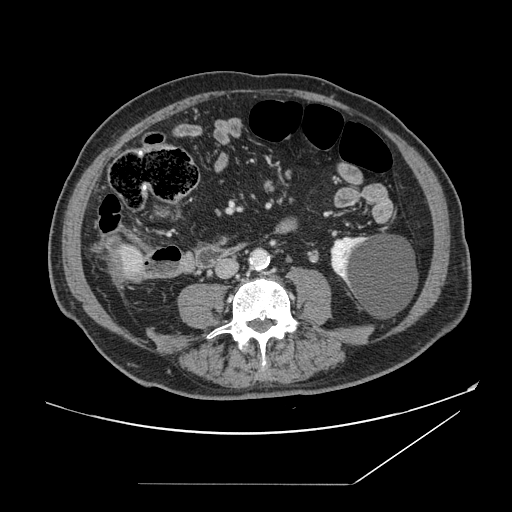
Contrast-enhanced abdominal CT, one axial slice. Slice 23 of 166 in the series (ordered by position). 120 kVp. Intravenous contrast given. Soft-tissue window (W 400 / L 40 HU). 2.5 mm slice thickness. 512 × 512 image matrix. Male patient, age 80 years. From the clinical record (not read from this slice): diagnosis: colorectal cancer liver metastases, imaged before liver resection; multiple liver metastases: no; largest metastasis: 2.2 cm; disease in both lobes: no.
Structures marked on this image (manually delineated by an expert):
- liver: bounding box (x1, y1, x2, y2) in pixels: (107, 242, 147, 281)
- liver metastasis: (111, 248, 129, 280)